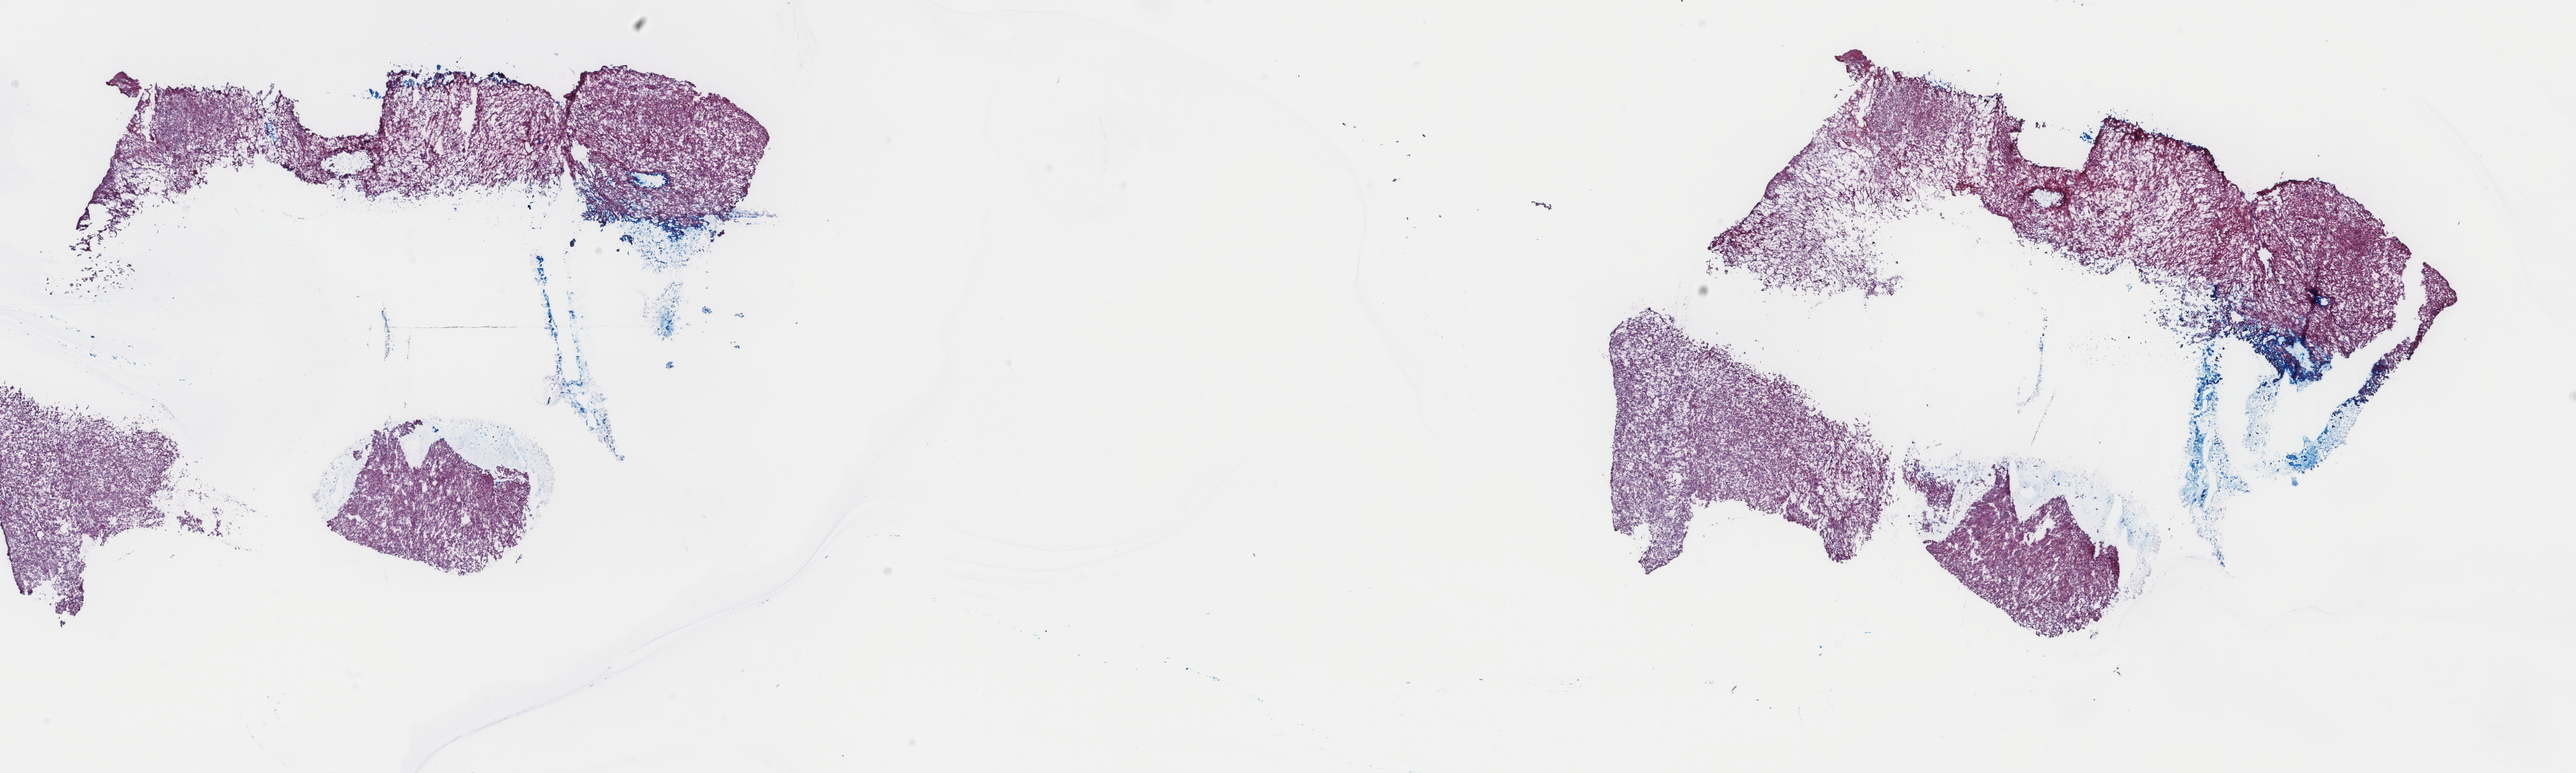
Digitized H&E tissue section (whole slide), whole scanned area (about 27.6 x 8.3 mm) shown as a low-resolution overview, frozen section, ovary, primary tumour sample. Female patient; age at initial diagnosis 65 years. Composition of this section per pathologist review: tumour cells 95%, tumour nuclei 100%, normal cells 0%, stromal cells 5%, necrosis 0%. Inflammatory infiltration, as recorded: lymphocyte infiltration 0%, monocyte infiltration 0%, neutrophil infiltration 0%.
* diagnosis: Leiomyosarcoma, NOS